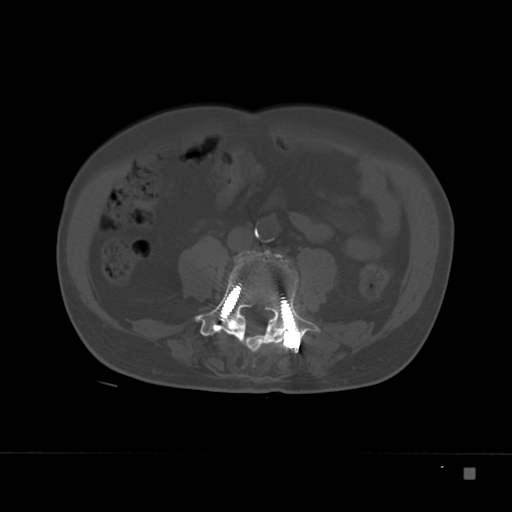
CT including the spine, one axial slice. Slice 48 of 332 in the series (ordered by position). 120 kVp. Bone window (W 1800 / L 400 HU). 1.5 mm slice thickness. 512 × 512 image matrix, field of view 389 × 389 mm. Male patient, age 72 years. Case-level facts recorded for this patient, not image findings: primary cancer: skeletal.
Annotated regions visible in this slice (semi-automatic segmentation, software-assisted and operator-edited):
- L4 vertebra: bounding box [x1, y1, x2, y2] px = [195, 250, 322, 352]